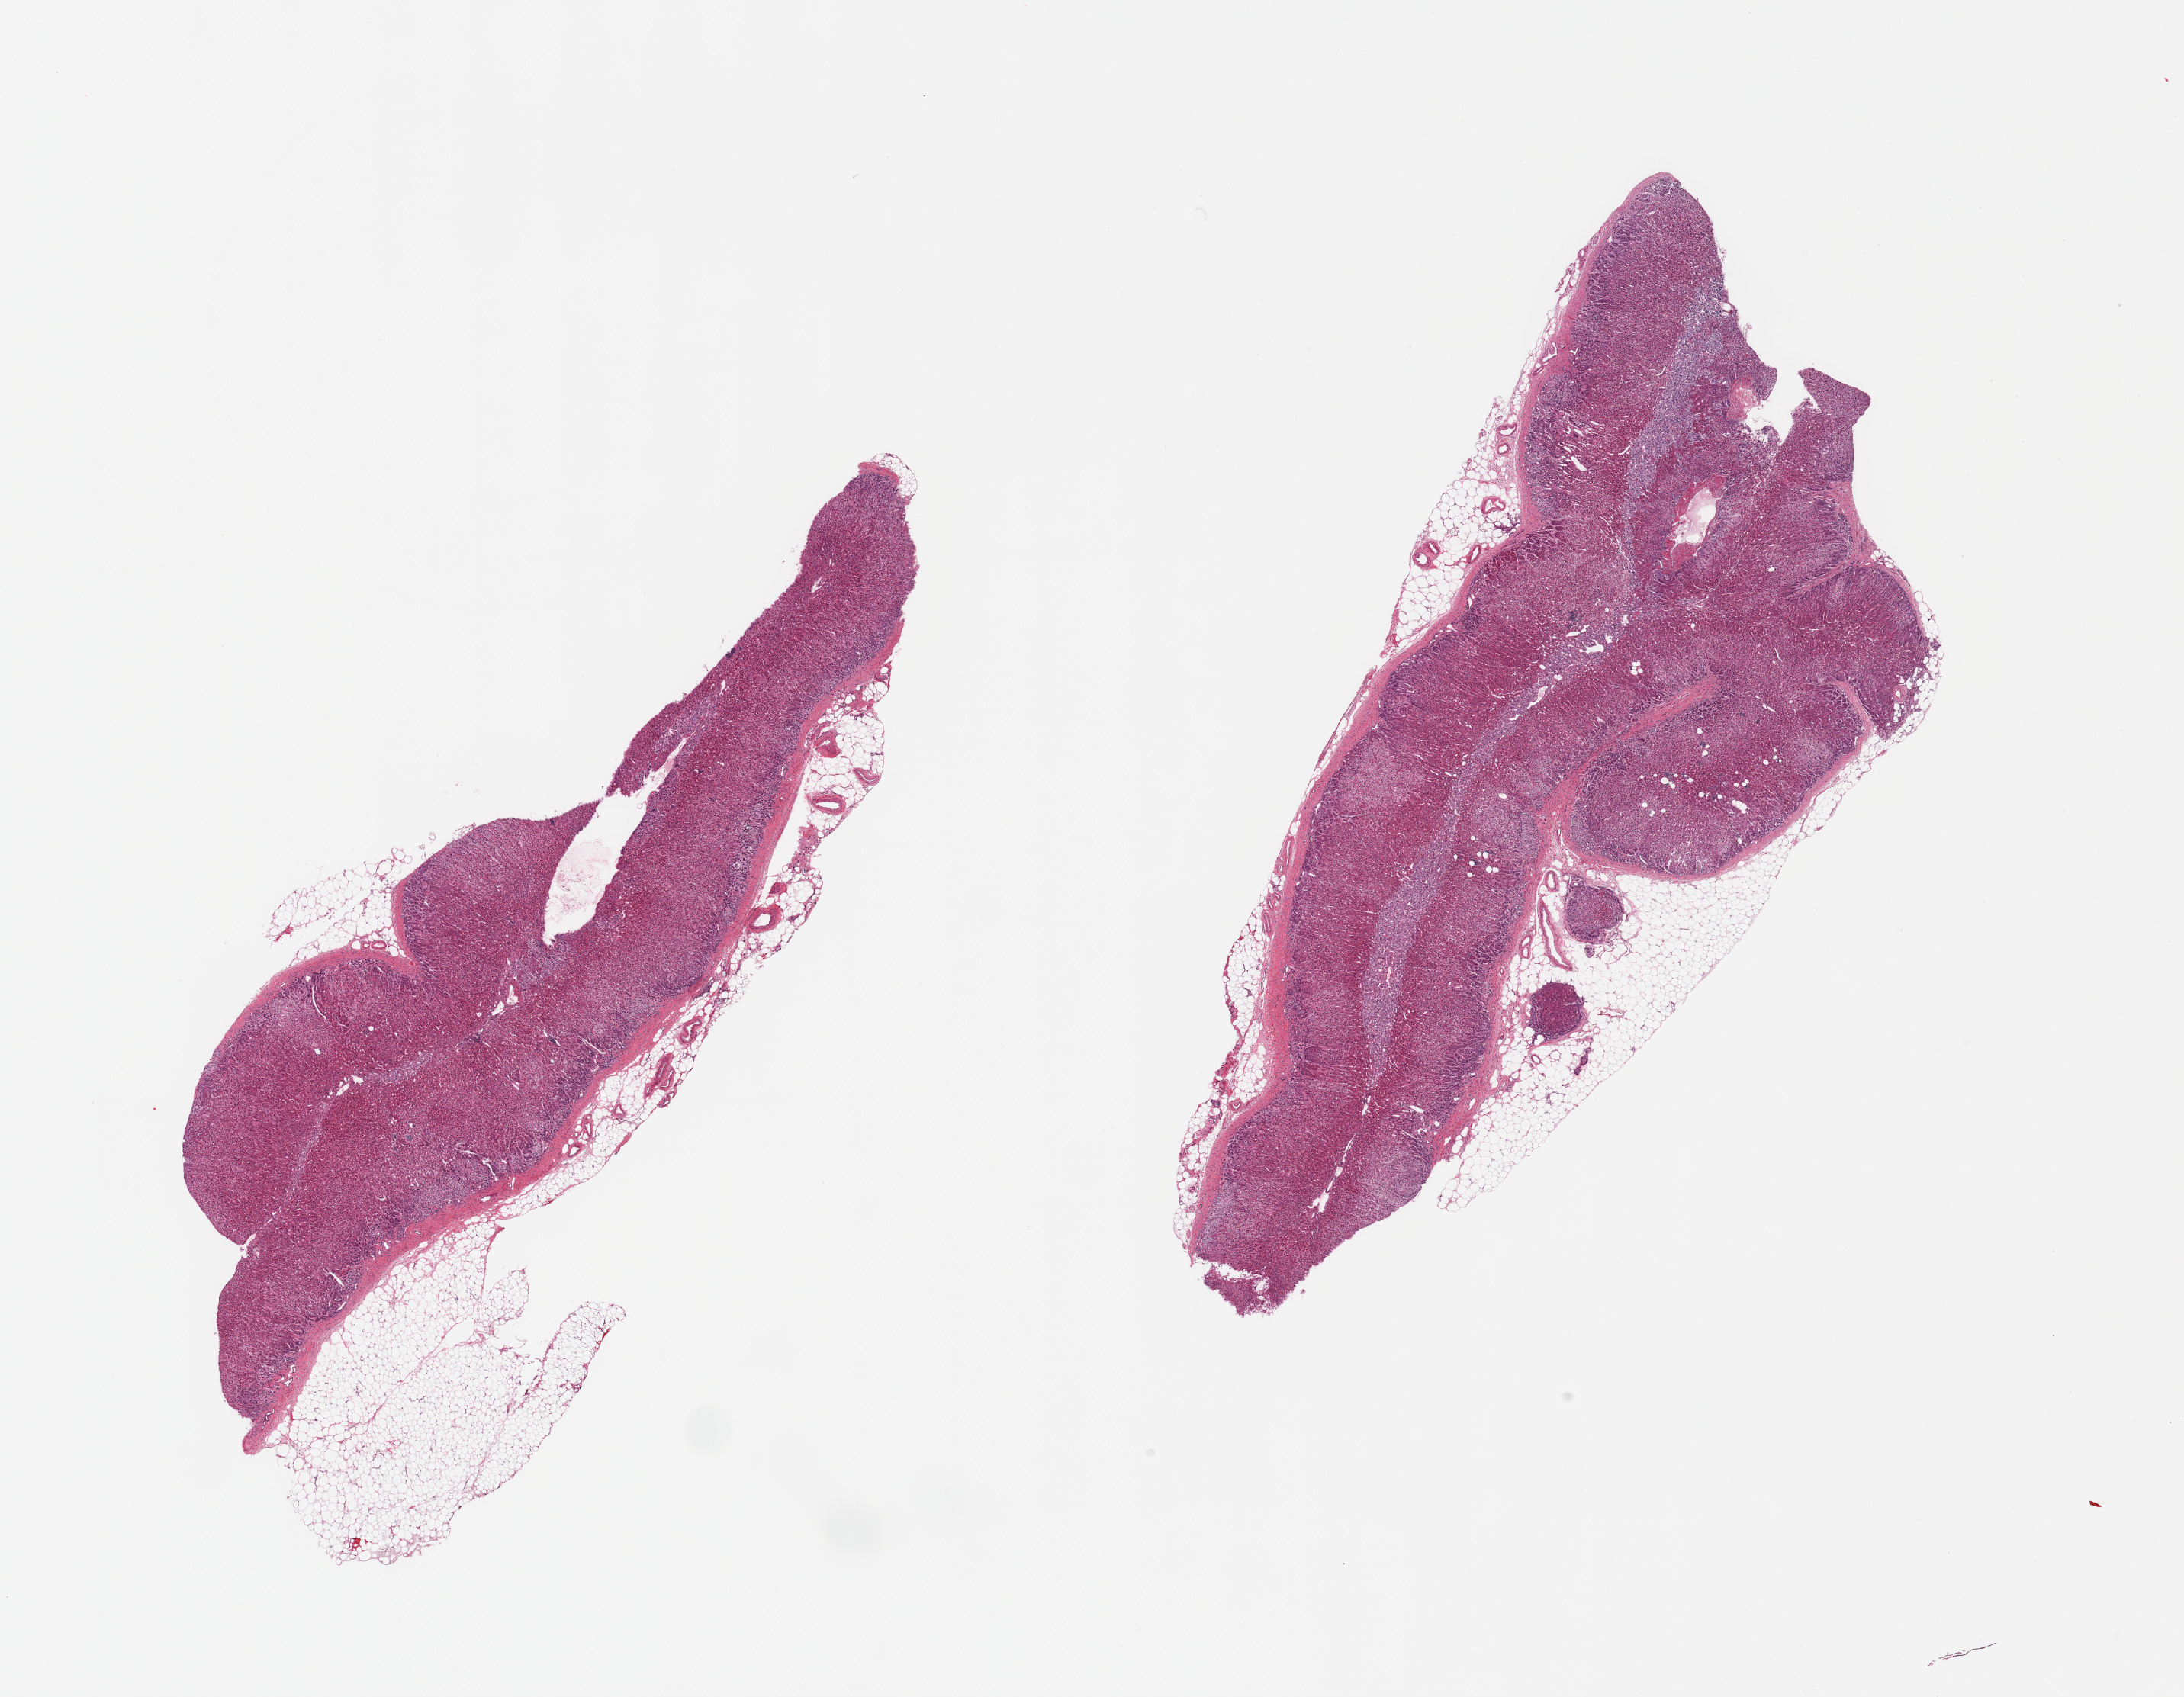
Digitized hematoxylin and eosin (H&E)-stained section, shown as a low-resolution overview of the whole scanned area (about 22.6 x 17.6 mm, slide scanned at 20x), PAXgene-fixed paraffin-embedded (PFPE) section, section of adrenal gland (target tissue), tissue donor sample. Female donor.
Review note (as recorded): 2 pieces, well fixed cortex and central medulla adherent nubbins of fat up to ~2mm.